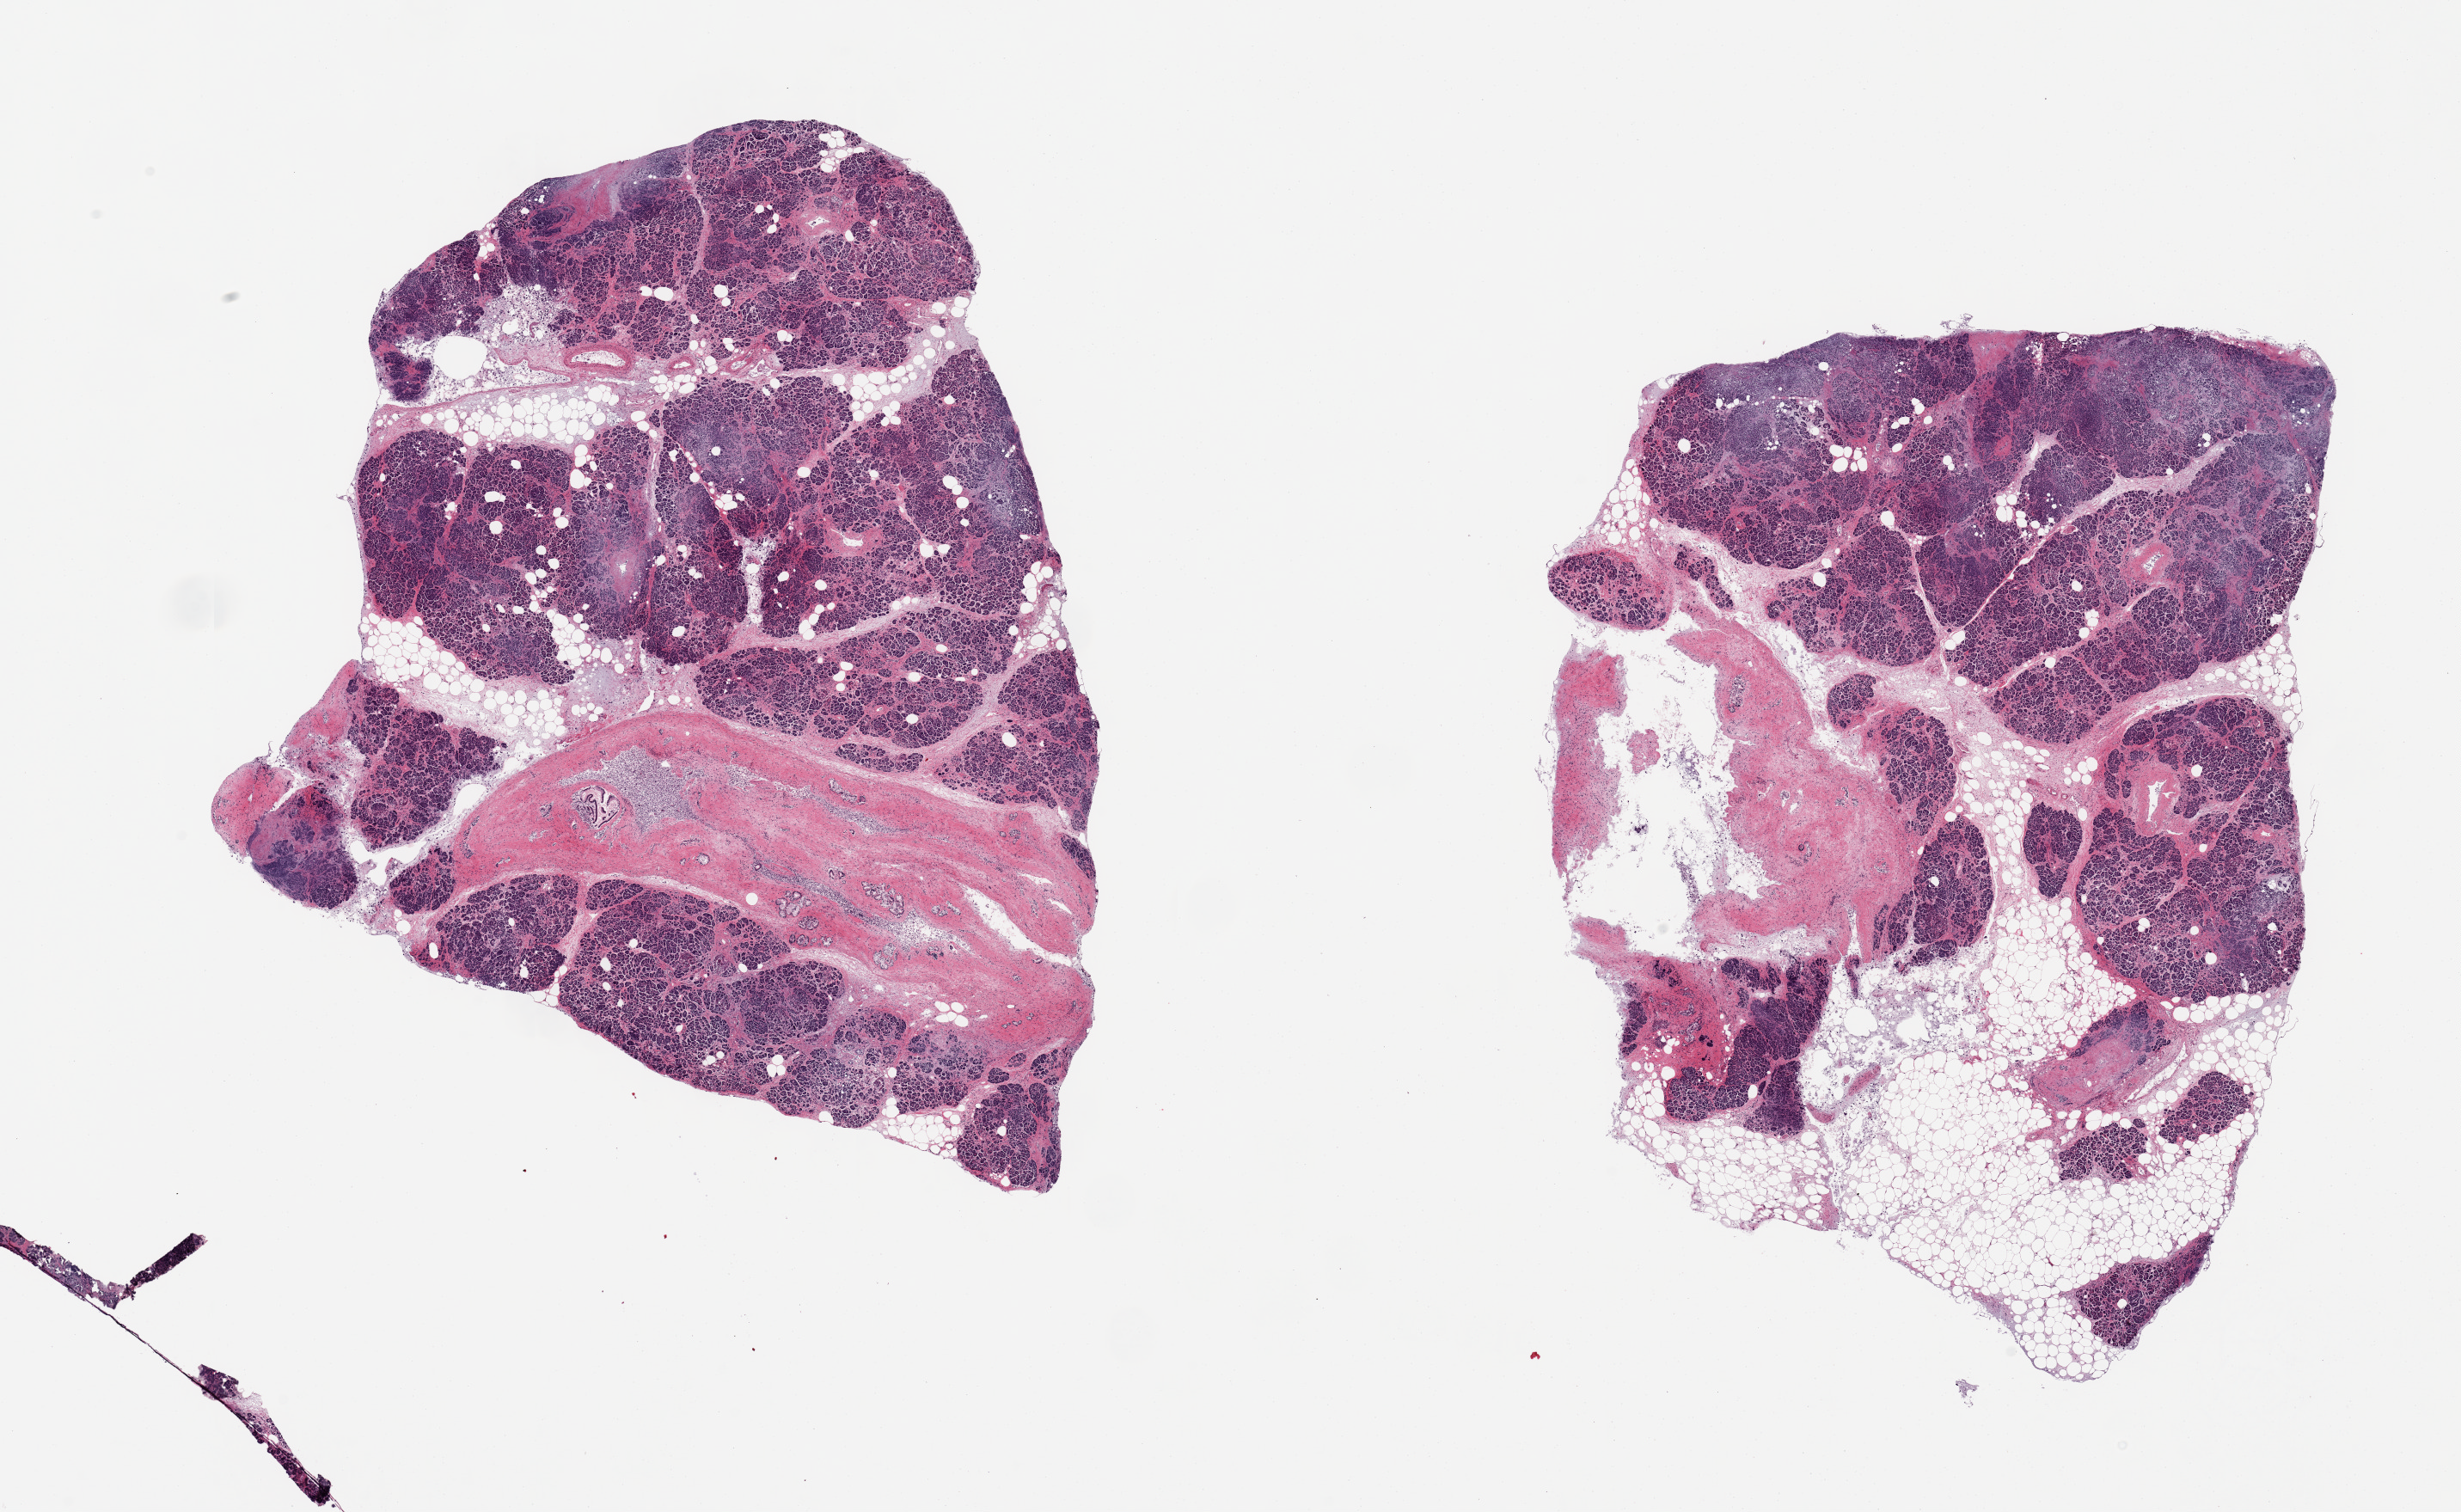
Hematoxylin and eosin (H&E) whole-slide image, brightfield — a low-resolution overview of the entire scanned area, about 22.6 x 13.9 mm (from a 20x scan); PAXgene-fixed paraffin-embedded (PFPE) section; target tissue: pancreas; donor tissue sample. Donor sex: male.
• review note (as recorded): 2 piece, moderate/advanced saponification. Islets degraded